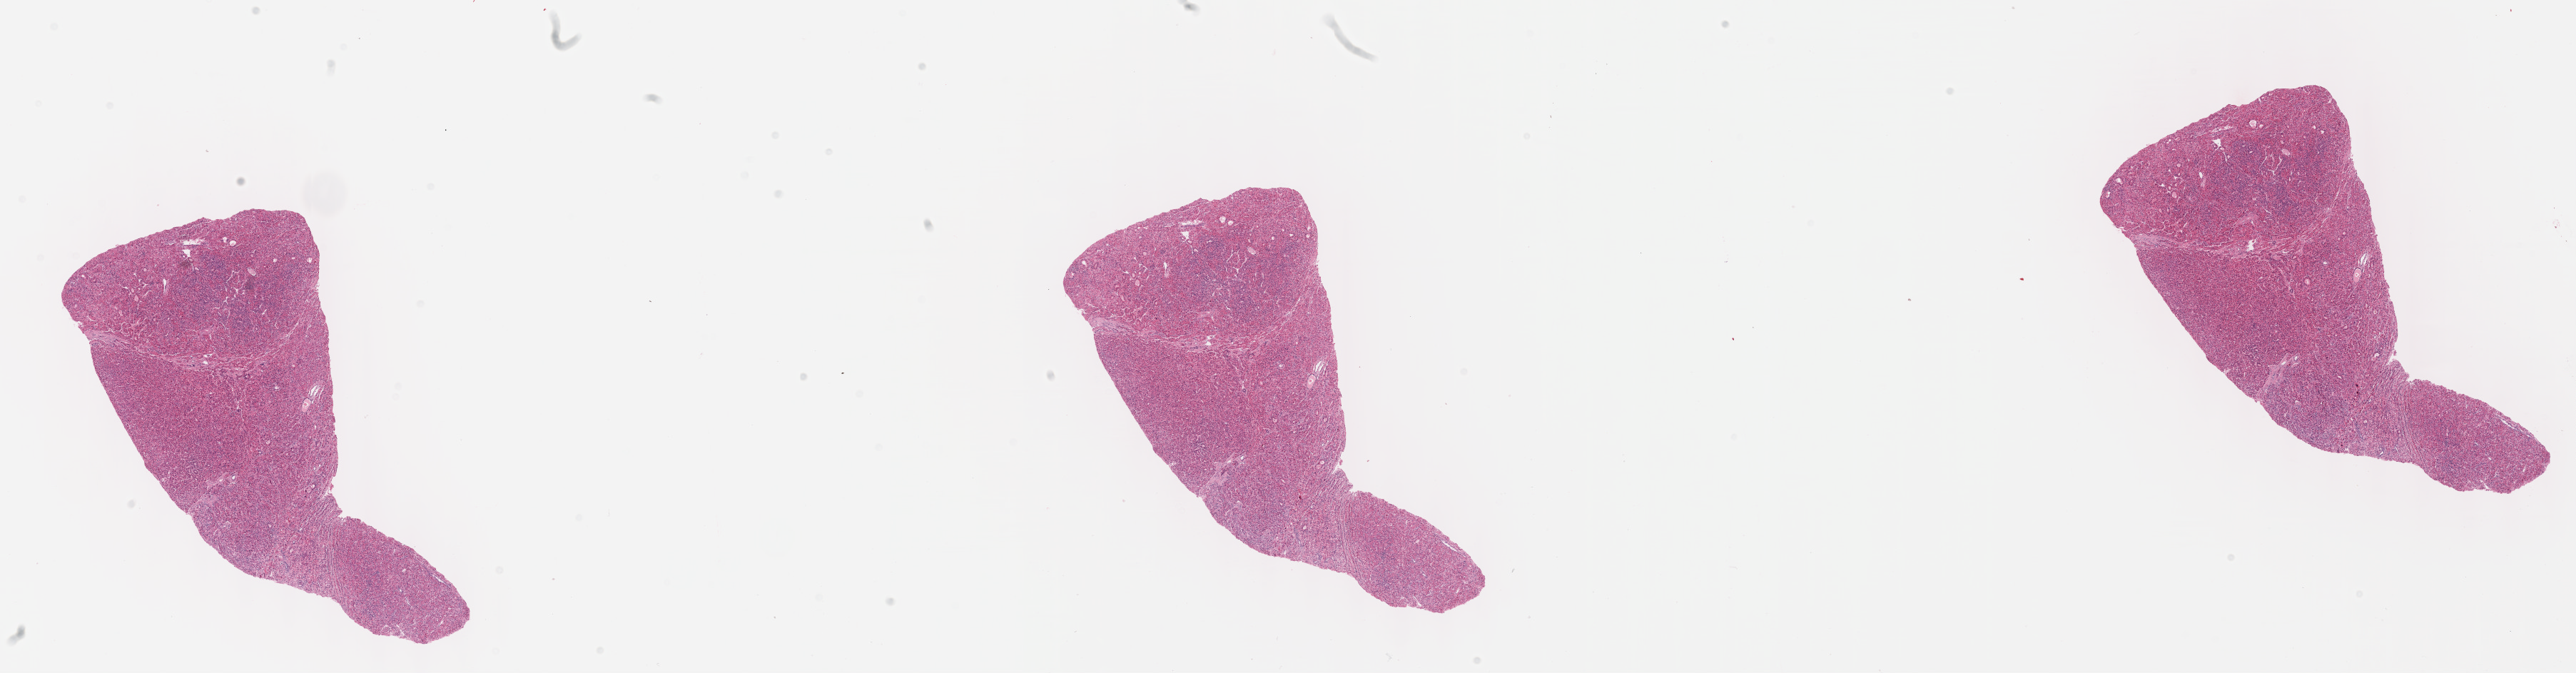
Digitized H&E-stained tissue section (whole slide), low-resolution overview of the scanned area, about 29.2 x 7.6 mm (slide scanned at 40x), formalin-fixed paraffin-embedded (FFPE) diagnostic section, sample: primary tumour, liver. Male, age 55 years at initial diagnosis. Histologic grade: G4 (undifferentiated).
* AJCC pathologic stage: I
* histologic diagnosis: Hepatocellular carcinoma, NOS